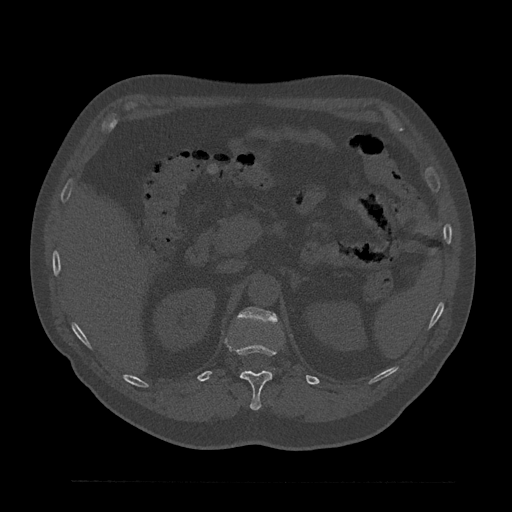
CT including the spine, one axial slice. Slice 209 of 797 in the series (ordered by position). 120 kVp. Bone window (W 1800 / L 400 HU). 0.5 mm slice thickness. 512 × 512 image matrix. Male patient, age 61 years. Case-level facts recorded for this patient, not image findings: primary cancer: prostate.
Annotated regions visible in this slice (semi-automatically segmented with operator editing):
- L1 vertebra: box from (x=237, y=307) to (x=277, y=323) px
- T12 vertebra: (x=225, y=339)–(x=283, y=410)